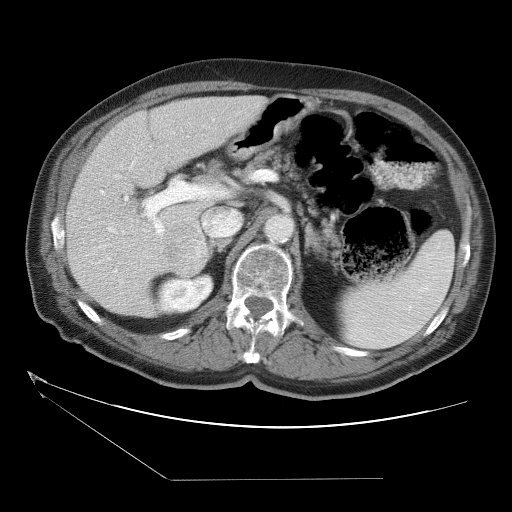
Contrast-enhanced abdominal CT (liver protocol), one axial slice. Slice 18 of 38 in the series (ordered by position). Reconstruction kernel STANDARD. One of 2 acquisitions stored at this slice position. Soft-tissue window (W 400 / L 40 HU). 5 mm slice thickness. 512 × 512 image matrix, field of view 400 × 400 mm. From the clinical record (not read from this slice): diagnosis: hepatocellular carcinoma (patient treated with transarterial chemoembolisation; whether this scan precedes or follows treatment is not stated here); TNM stage (as recorded): Stage-II; Child-Pugh class: A; tumour nodularity: multinodular.
Outlined on this slice (semi-automatic segmentation, software-assisted and operator-edited):
- liver parenchyma outside the tumour (the mass and vessels are separate outlines, so this box may not span the whole liver): bounding box (x1, y1, x2, y2) in pixels: (66, 96, 267, 316)
- mass: (162, 219, 211, 277)
- liver vessels: (87, 190, 164, 299)